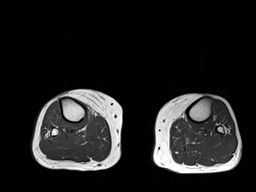
MRI of an extremity soft-tissue mass, one axial slice; slice 20 of 32 in the series (ordered by position); 6 mm slice thickness; 256 × 192 image matrix, field of view 375 × 281 mm. Female patient. From the clinical record (not read from this slice): histological type: undifferentiated – high grade; grade: high; site of the primary tumour: right thigh.
Annotated regions visible in this slice (manually delineated by an expert):
- gross tumour volume (mass): bounding box <85,110,96,122> (left, top, right, bottom; pixels)